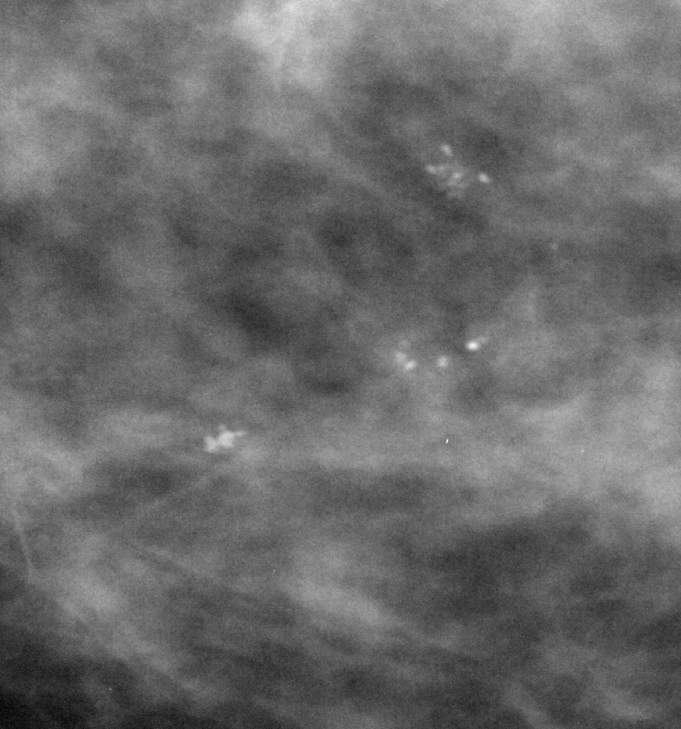
Cropped region of a digitized screen-film mammogram centred on a radiologist-marked abnormality; right breast; CC view; BI-RADS breast density category 3 (scale 1–4).
- Finding: calcifications, morphology pleomorphic, distribution clustered; BI-RADS assessment category 4; pathology (as recorded): benign.